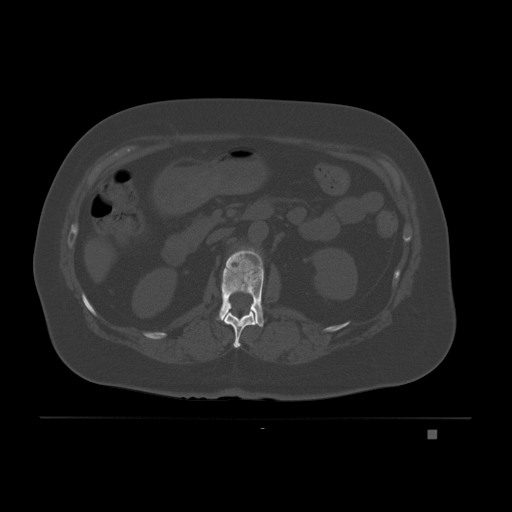
CT including the spine, one axial slice; position 74 of 221 along the scan axis; bone window (W 1800 / L 400 HU); 3 mm slice thickness; 512 × 512 image matrix, field of view 474 × 474 mm. Patient: female, 63 years. Case-level facts recorded for this patient, not image findings: primary cancer: breast.
Annotated regions visible in this slice (semi-automatically segmented with operator editing):
- L1 vertebra: box from (x=217, y=247) to (x=265, y=327) px
- T12 vertebra: (x=224, y=309)–(x=257, y=348)